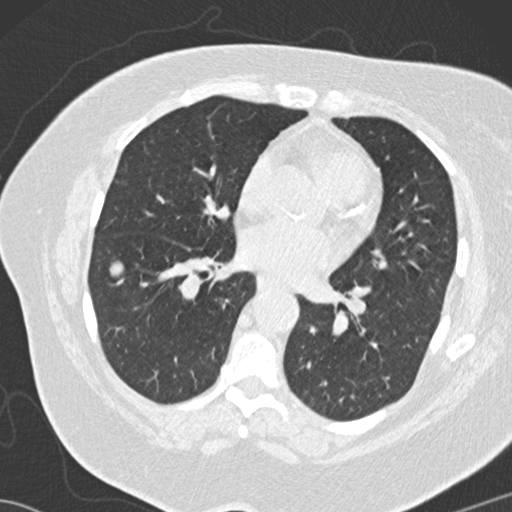
Low-dose screening chest CT, one axial slice; slice 66 of 146 in the series (ordered by position); reconstruction kernel B30f; lung window (W 1500 / L -600 HU); 2 mm slice thickness; 512 × 512 image matrix.
Annotated regions visible in this slice (outlined manually by an expert reader):
- lesion 2 (tumor, lower lobe of right lung): bounding box (x1, y1, x2, y2) in pixels: (108, 261, 125, 278)